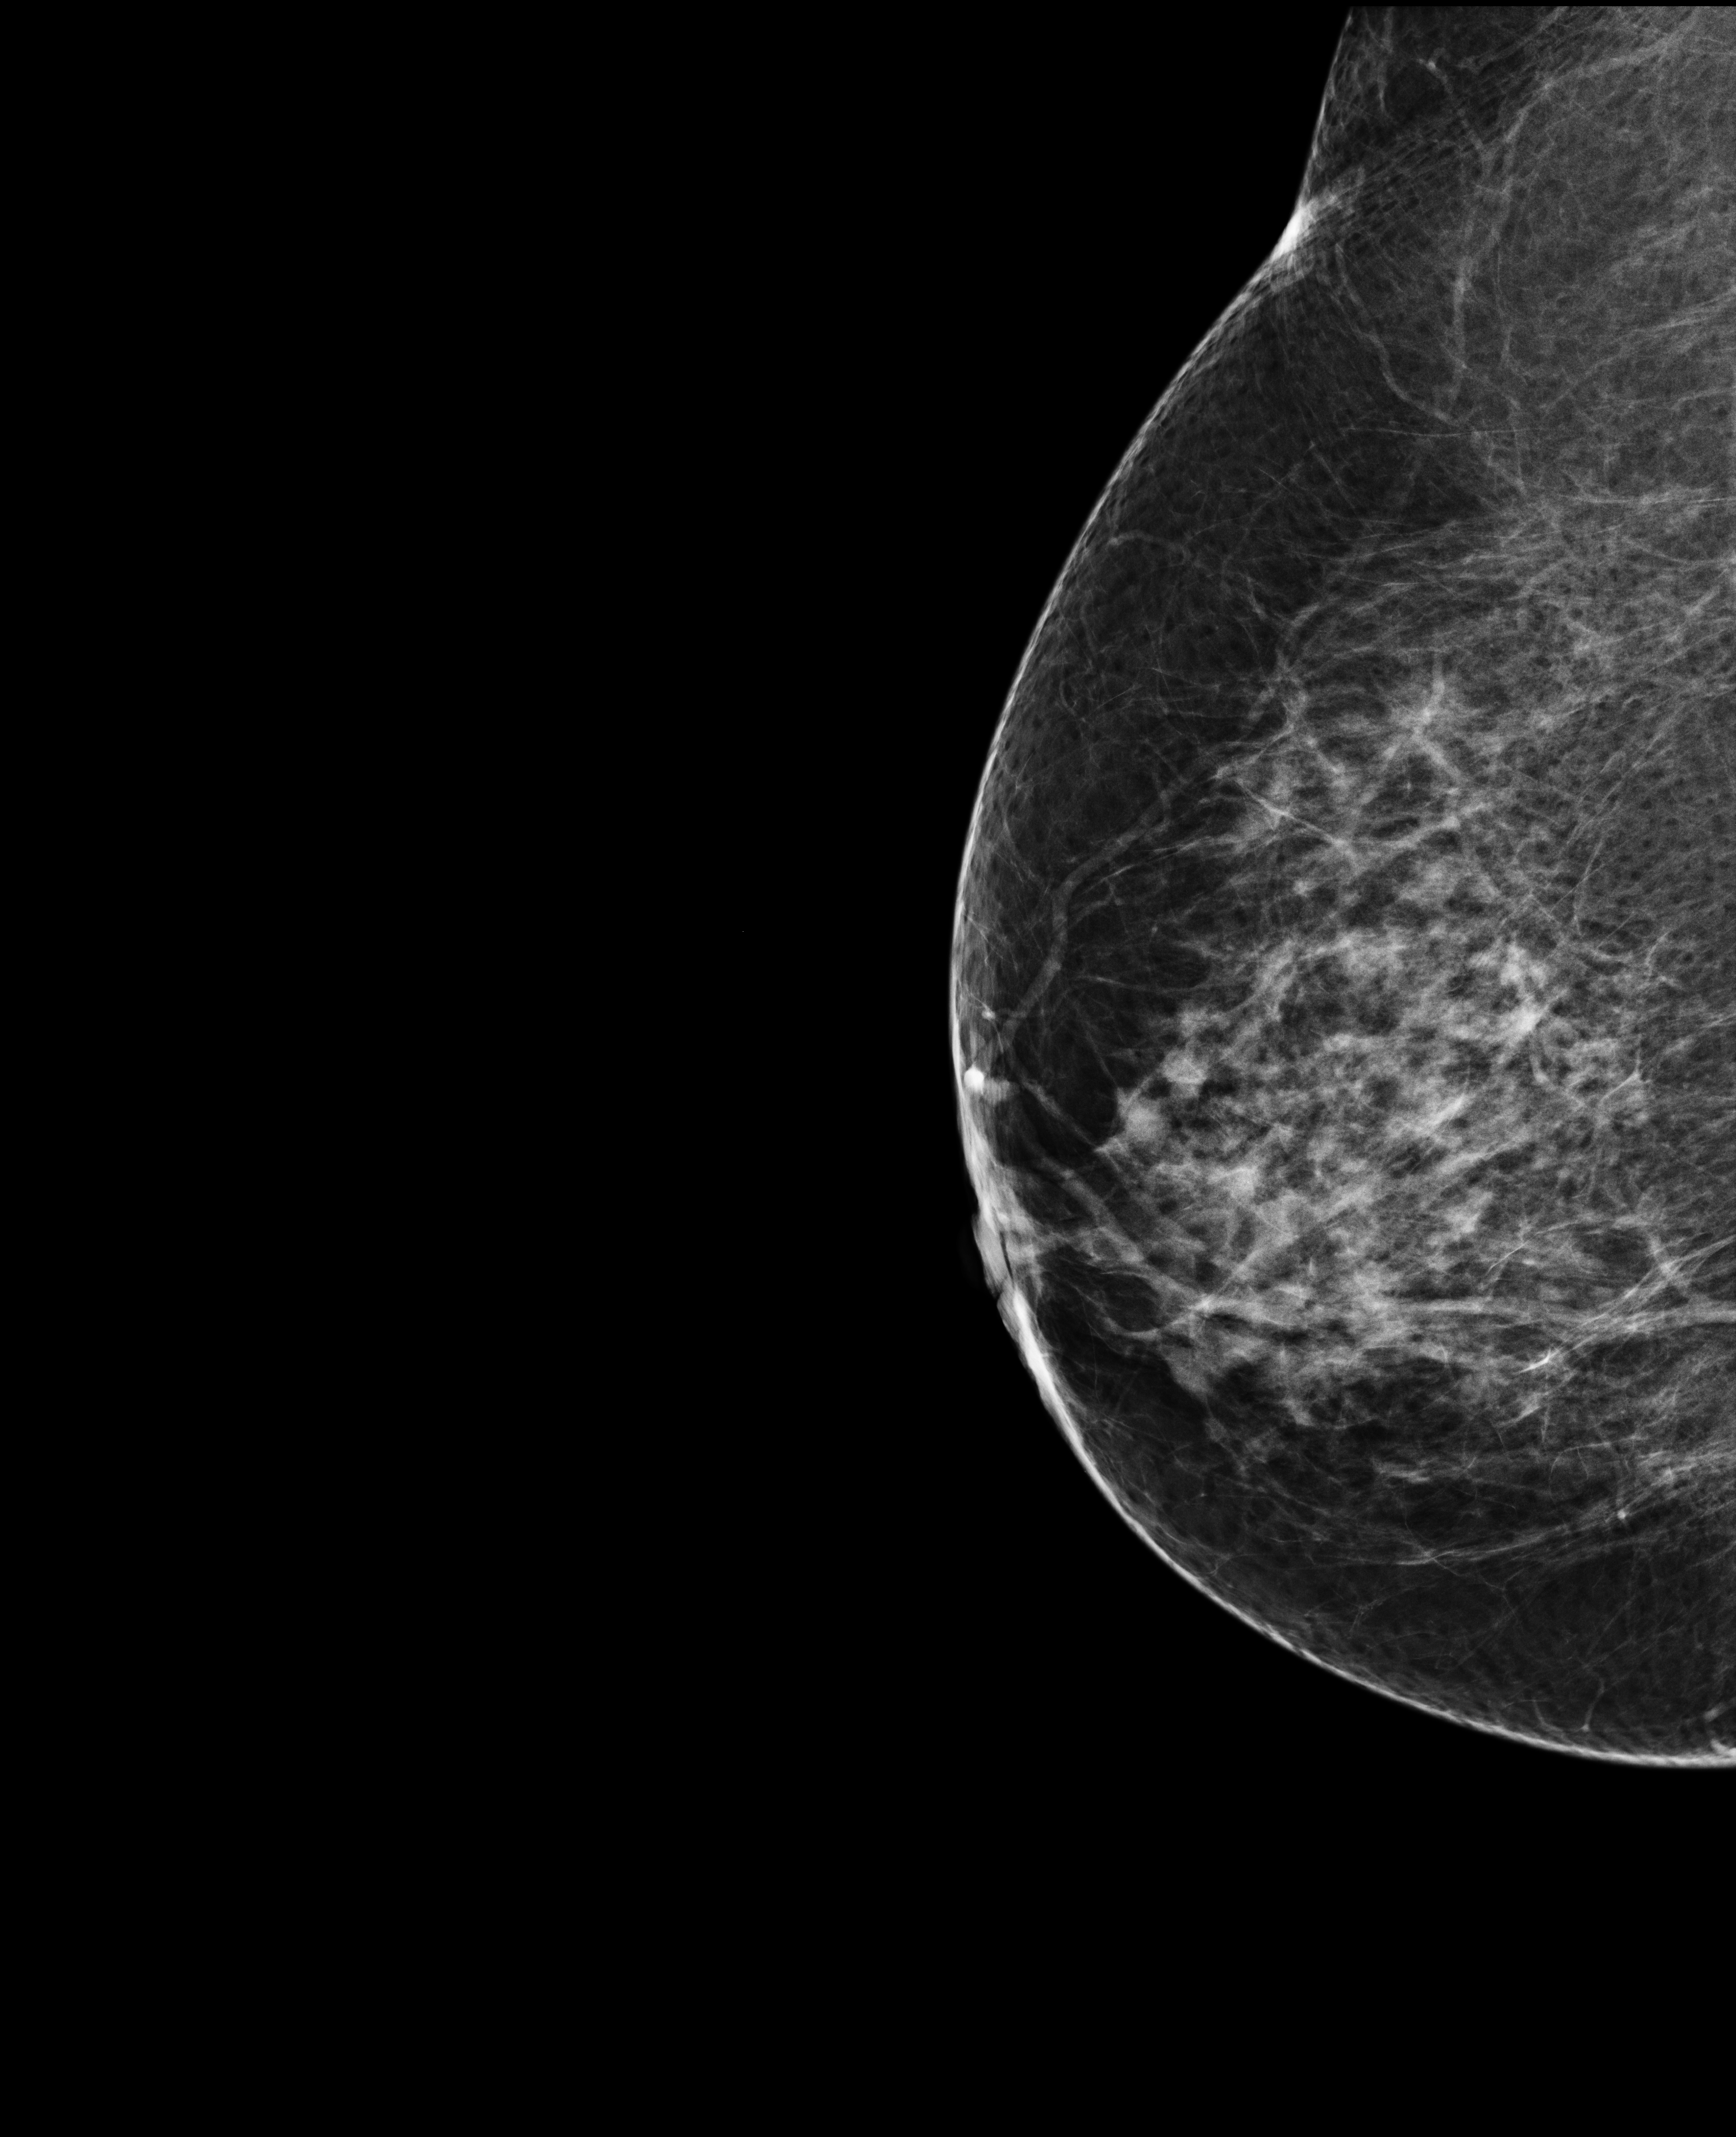
Full-field digital mammogram (FFDM); right breast; exaggerated CC view (lateral); screening examination. Patient aged 71 years (female).
Breast density at the screening exam (both breasts): heterogeneously dense (BI-RADS density category c). Final BI-RADS assessment for this screening round (tomosynthesis exam, both breasts): category 2. Recall: no recall after this screen.